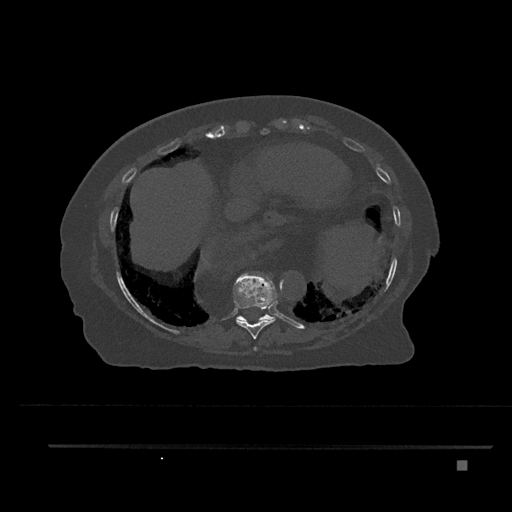
CT including the spine, one axial slice; slice 386 of 797 in the series (ordered by position); reconstruction kernel Br40s/3; 120 kVp; bone window (W 1800 / L 400 HU); 512 × 512 image matrix, field of view 437 × 437 mm. Patient: female, 76 years. Case-level facts recorded for this patient, not image findings: primary cancer: lung; vertebrae with lytic lesions (as recorded): T11, L3.
Outlined on this slice (semi-automatic segmentation, software-assisted and operator-edited):
- T10 vertebra: bounding box <236,314,275,322> (left, top, right, bottom; pixels)
- T8 vertebra: <253,347,257,351>
- T9 vertebra: <233,273,277,339>